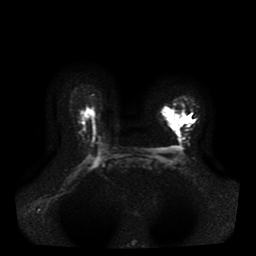
Breast MRI, one axial slice. Slice 28 of 41 in the series (ordered by position). Diffusion-weighted series; image 2 of 4 stored at this slice position (different b-values; order by instance number). 1.5 T. 5 mm slice thickness. 256 × 256 image matrix, field of view 330 × 330 mm. Female patient.
Annotated regions visible in this slice (outlined manually by an expert reader):
- tumour on diffusion-weighted imaging: box from (x=161, y=110) to (x=185, y=136) px